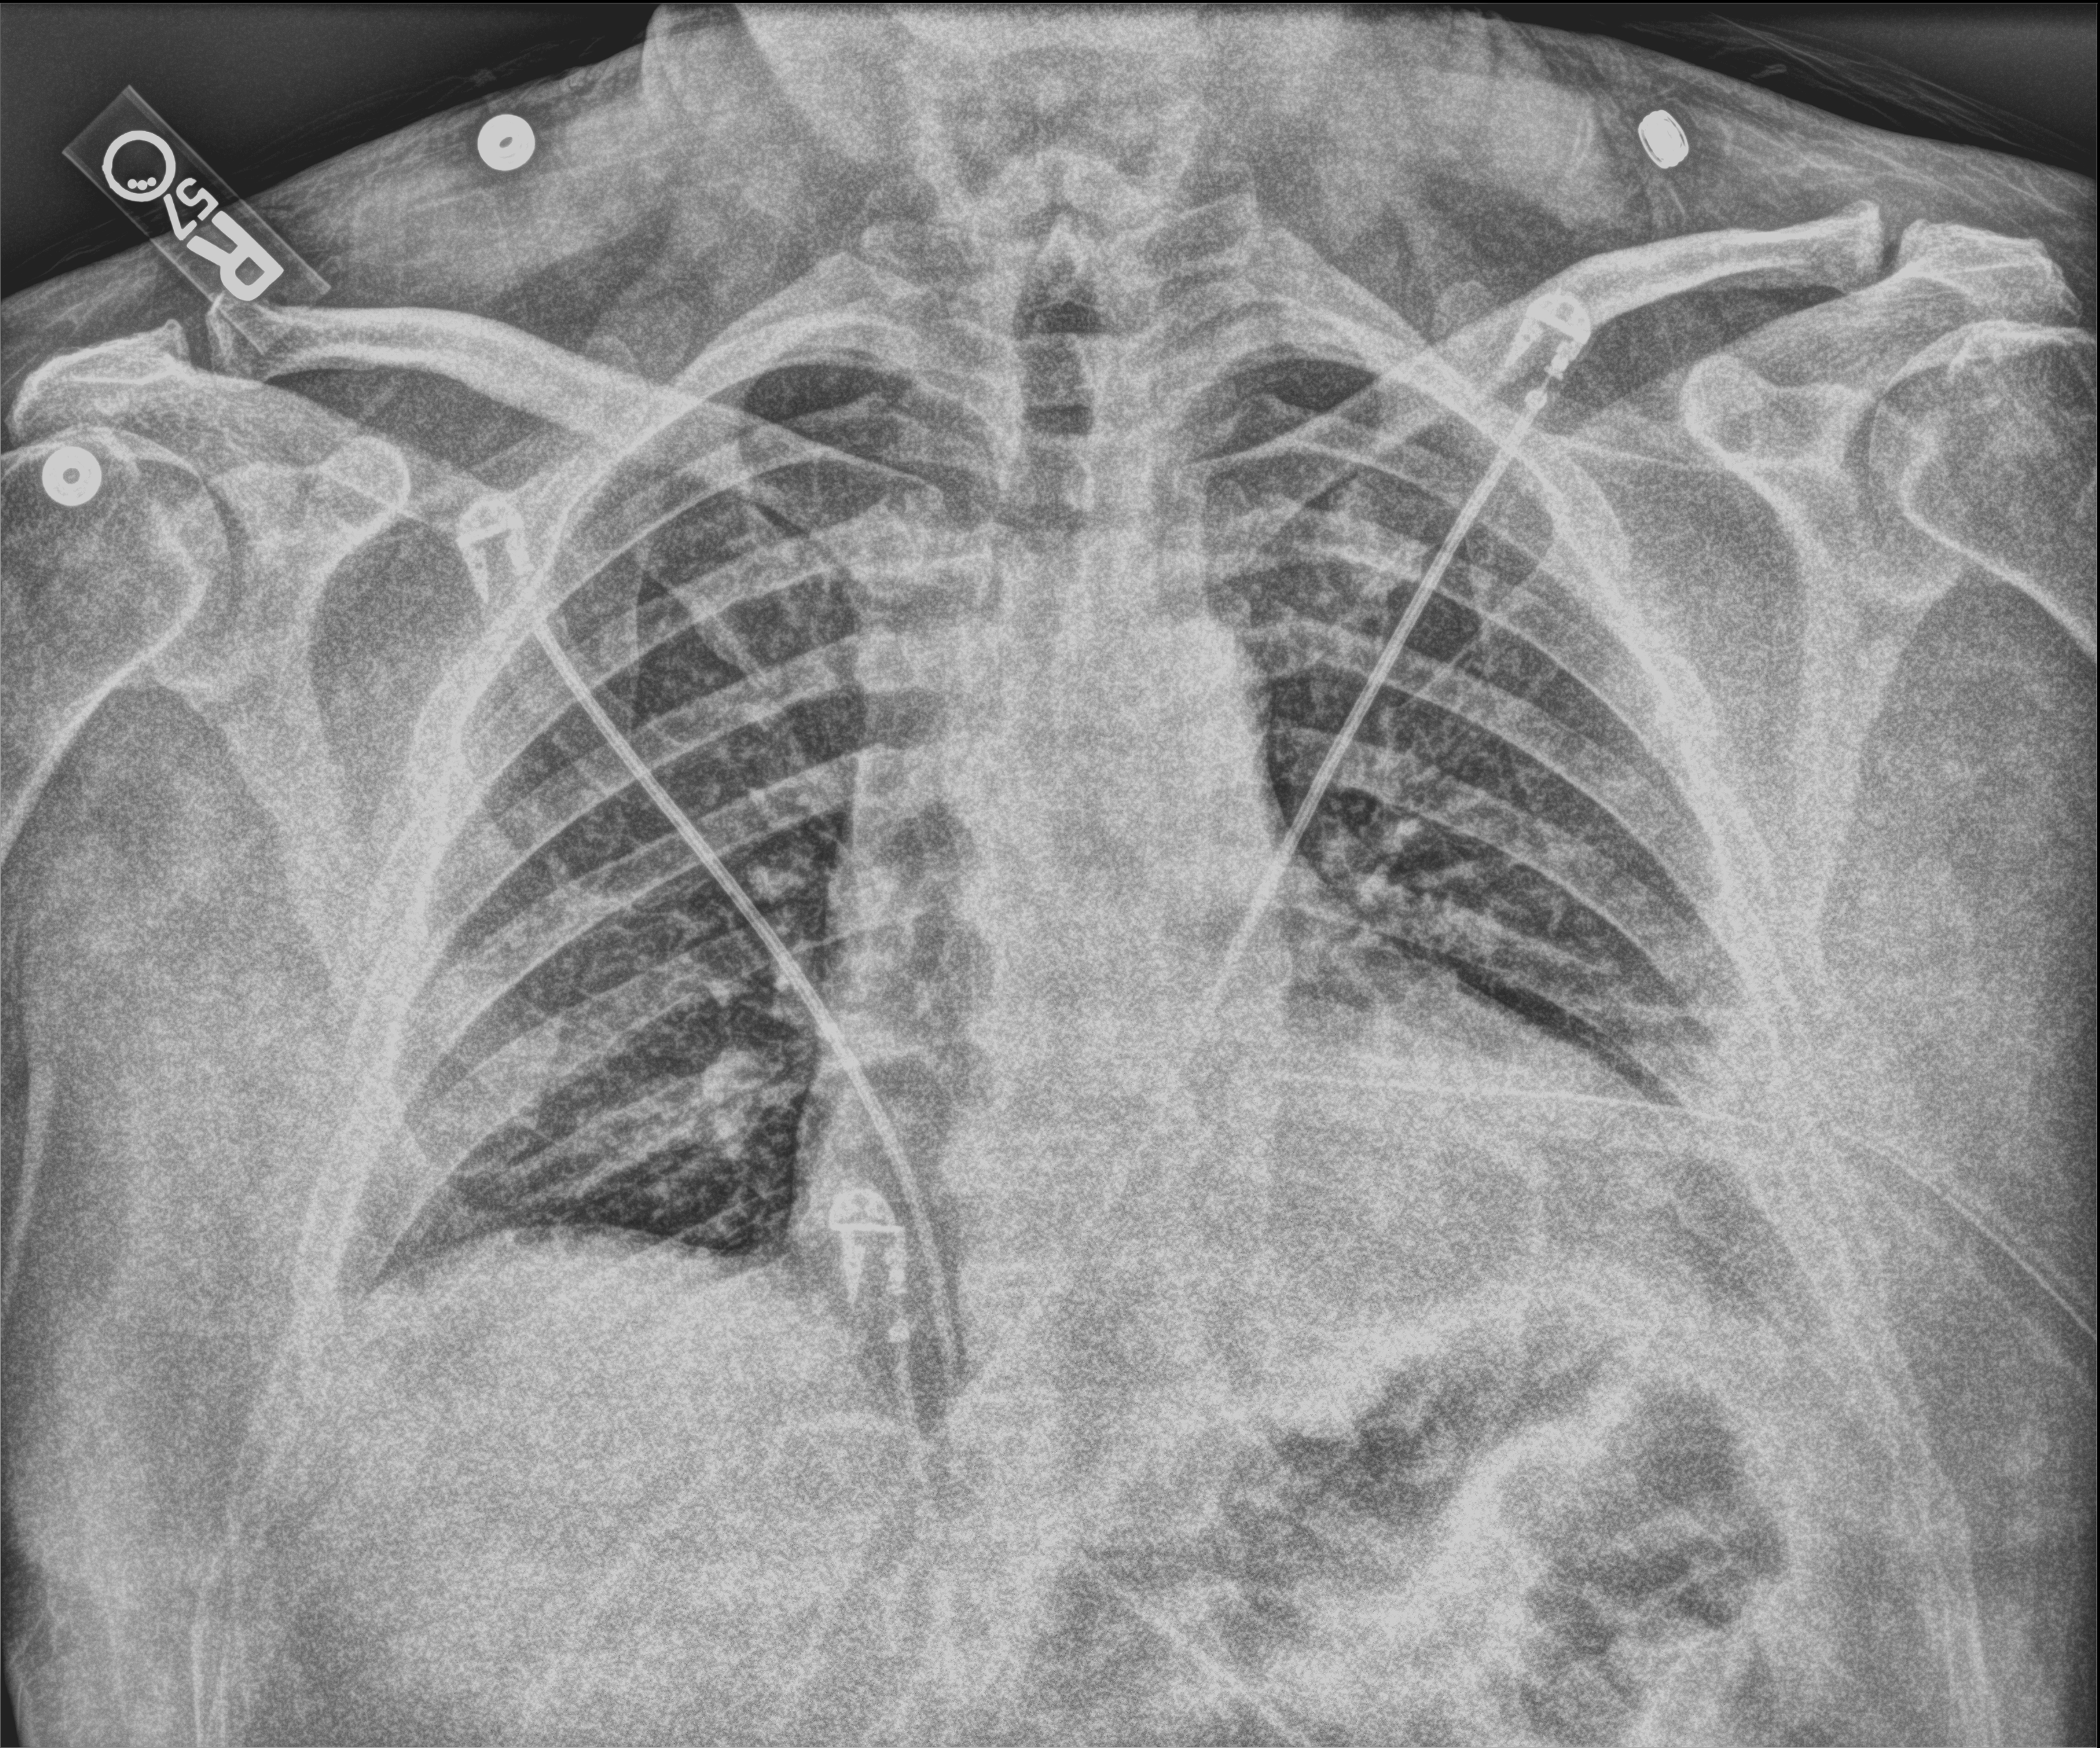
Bedside chest radiograph (computed radiography), anteroposterior (AP) projection. Patient hospitalised with COVID-19; male, aged 18–59 years.
Admission-level facts for this patient (not findings on this image; timing relative to this image not recorded):
- mechanically ventilated during this hospital stay: no
- admitted to intensive care during this hospital stay: no
- length of hospital stay: 10 days